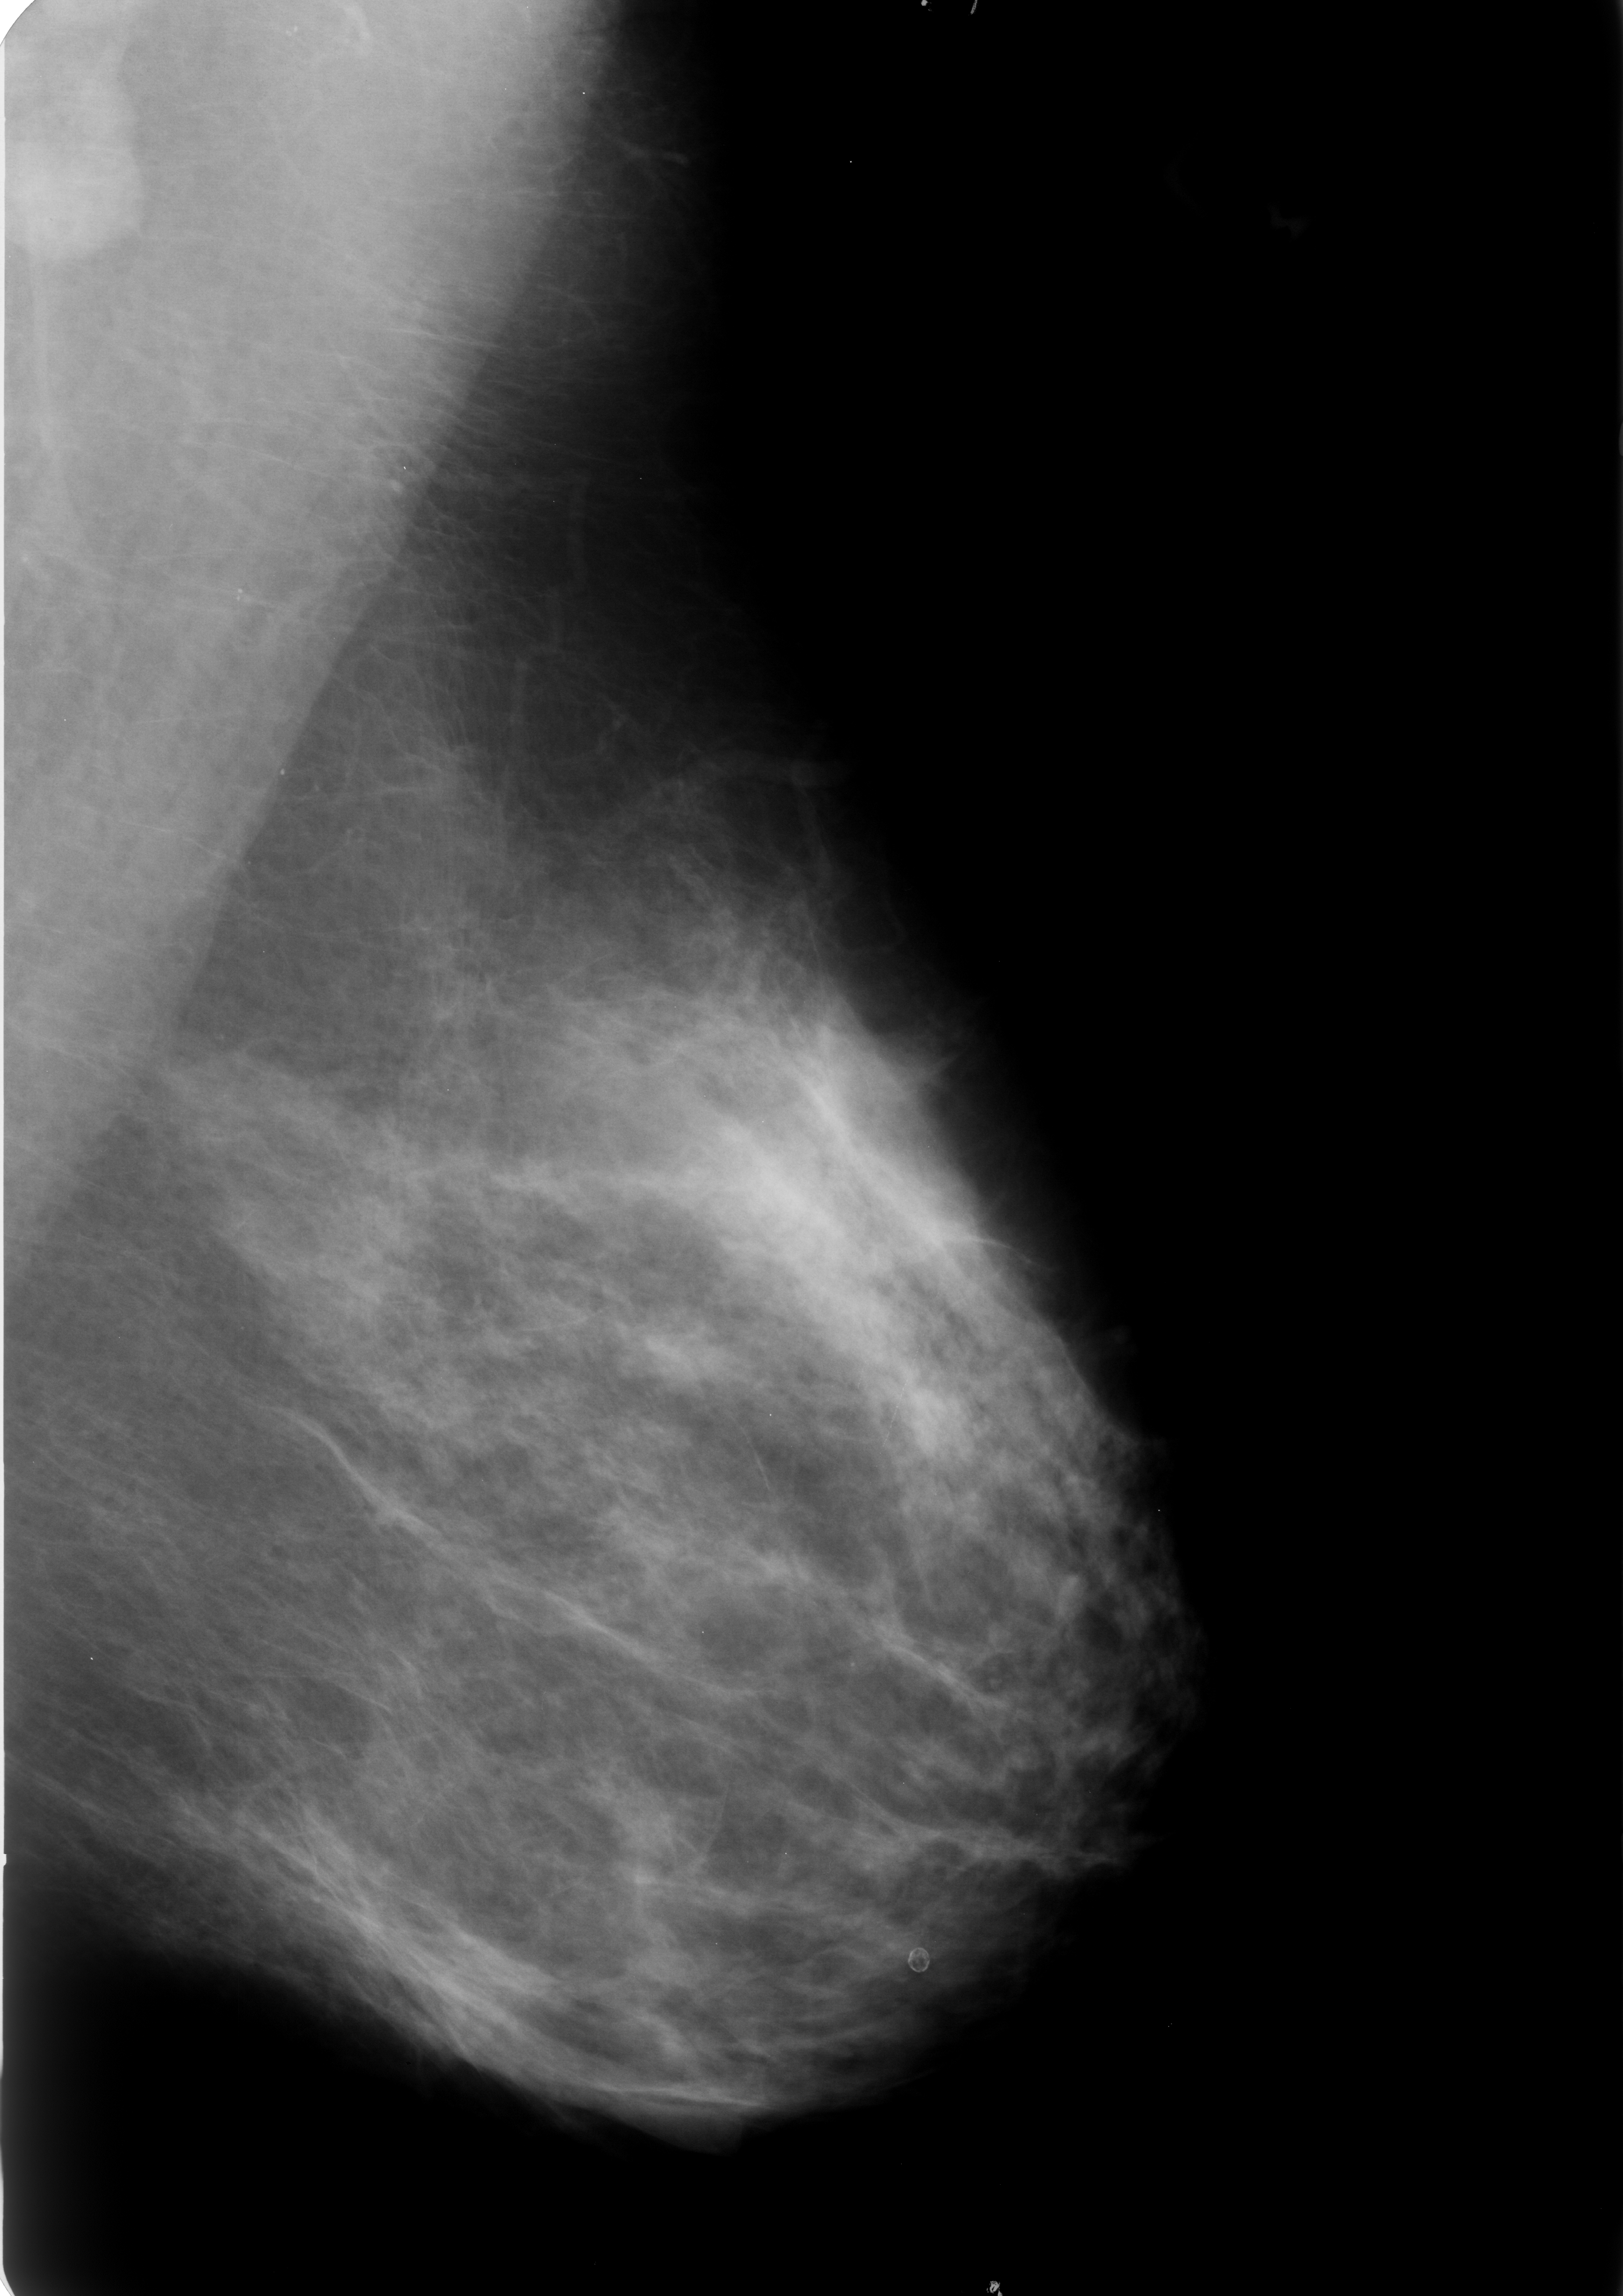
Mammogram (digitized film). Left breast. MLO view. Breast composition: scattered fibroglandular densities (BI-RADS density category 2 of 4). 1623 × 2296 image matrix.
Expert-marked regions of interest on this image (one box per marked abnormality):
- calcifications, morphology lucent center; BI-RADS assessment category 2; benign; no additional work-up was recommended (outcome (as recorded, no biopsy): benign without callback): bounding box (x1, y1, x2, y2) in pixels: (870, 1919, 947, 2000)